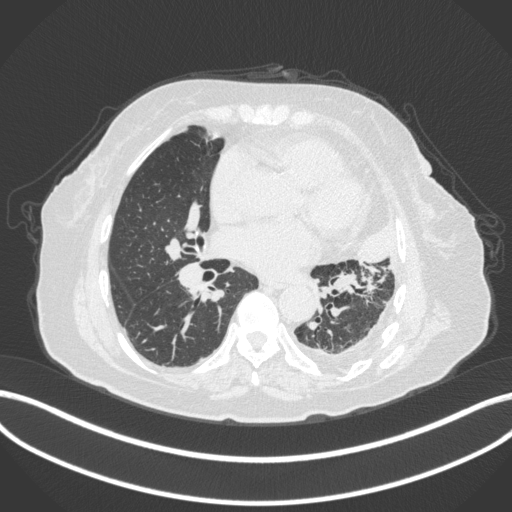
Chest CT, one axial slice; slice 173 of 399 in the series (ordered by position); 120 kVp; lung window (W 1500 / L -600 HU); 1 mm slice thickness; 512 × 512 image matrix, field of view 400 × 400 mm. Female patient, age 75 years. From the clinical record (not read from this slice): clinical TNM (as recorded): T3 N3 M1.
Outlined on this slice (bounding box drawn by a radiologist):
- lung tumour (recorded histology: adenocarcinoma): box from (x=355, y=213) to (x=396, y=265) px